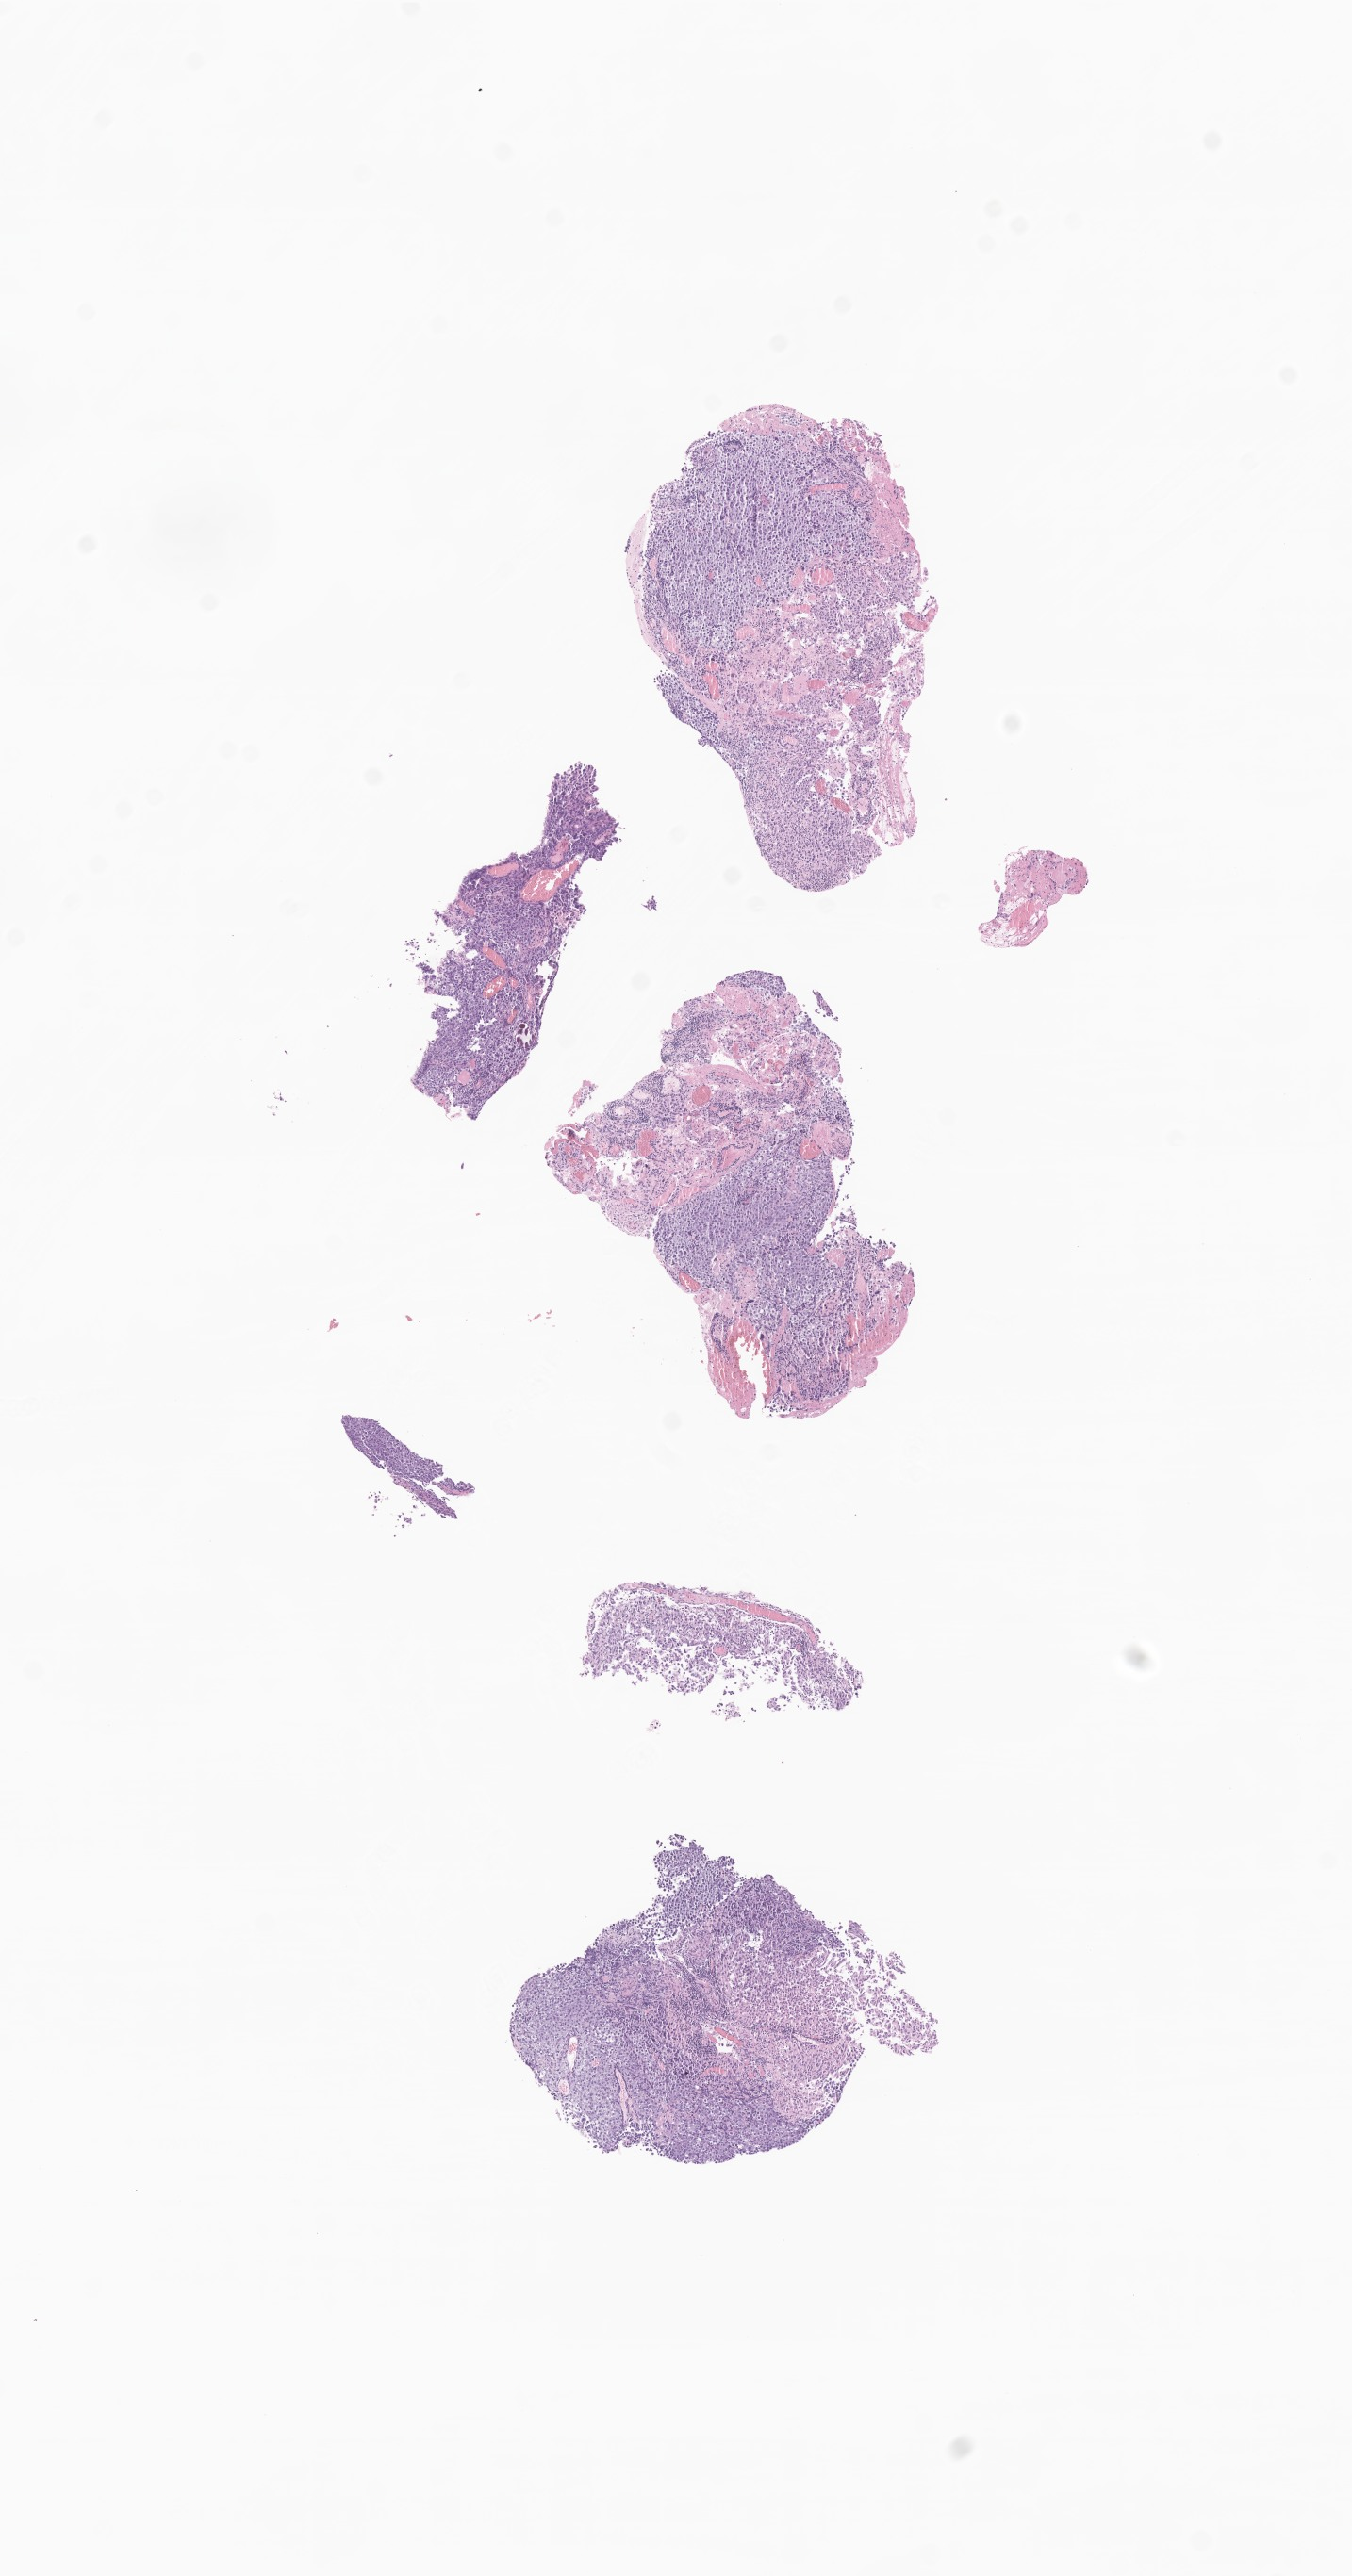
Whole-slide image, hematoxylin and eosin (H&E) stain of tumor tissue from the brain — shown as a low-resolution overview of the whole scanned area (about 6.0 x 11.5 mm). Formalin-fixed, paraffin-embedded (FFPE) tissue. Patient male; age 203 months (16 years 11 months).
Recorded diagnosis: Neoplasm, uncertain whether benign or malignant.